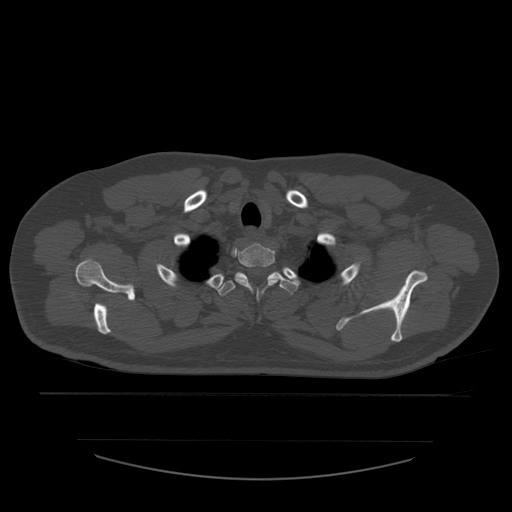
CT including the spine, one axial slice. Slice 460 of 532 in the series (ordered by position). 120 kVp. Bone window (W 1800 / L 400 HU). 1.25 mm slice thickness. 512 × 512 image matrix, field of view 441 × 441 mm. Patient age 44 years. From the clinical record (not read from this slice): primary cancer: soft tissue sarcoma.
Annotated regions visible in this slice (semi-automatically segmented with operator editing):
- T1 vertebra: box from (x=235, y=243) to (x=283, y=294) px
- T2 vertebra: (x=217, y=272)–(x=299, y=297)